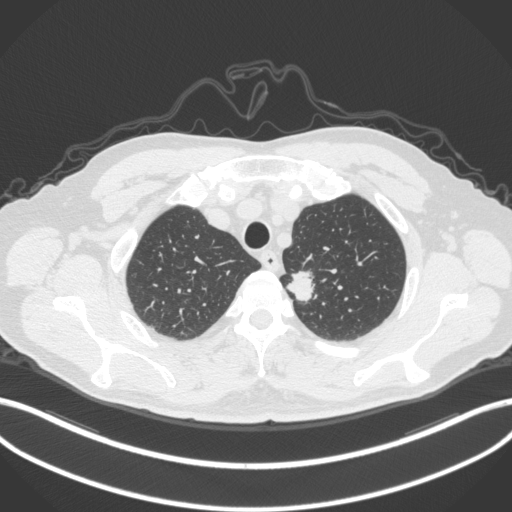
Chest CT, one axial slice; slice 318 of 382 in the series (ordered by position); 120 kVp; lung window (W 1500 / L -600 HU); 512 × 512 image matrix, field of view 400 × 400 mm. Male patient, age 64 years. Case-level facts recorded for this patient, not image findings: clinical TNM (as recorded): T1c N0 M0.
Annotated regions visible in this slice (rectangle marked by the reading radiologist):
- lung tumour (recorded histology: adenocarcinoma): bounding box [x1, y1, x2, y2] px = [283, 261, 318, 306]